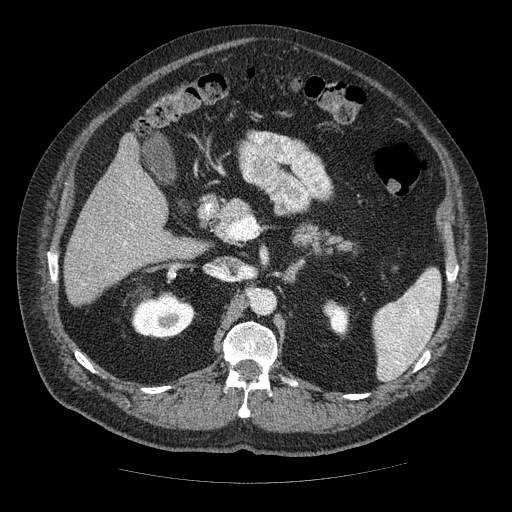
Contrast-enhanced abdominal CT (liver protocol), one axial slice. Position 23 of 85 along the scan axis. 120 kVp. Soft-tissue window (W 400 / L 40 HU). 512 × 512 image matrix, field of view 420 × 420 mm. From the clinical record (not read from this slice): diagnosis: hepatocellular carcinoma (patient treated with transarterial chemoembolisation; whether this scan precedes or follows treatment is not stated here); TNM stage (as recorded): Stage-IIIA; Child-Pugh class: A; tumour nodularity: multinodular.
Outlined on this slice (semi-automatically segmented with operator editing):
- liver parenchyma outside the tumour (the mass and vessels are separate outlines, so this box may not span the whole liver): bounding box (x1, y1, x2, y2) in pixels: (64, 134, 203, 304)
- liver vessels: (123, 183, 139, 246)